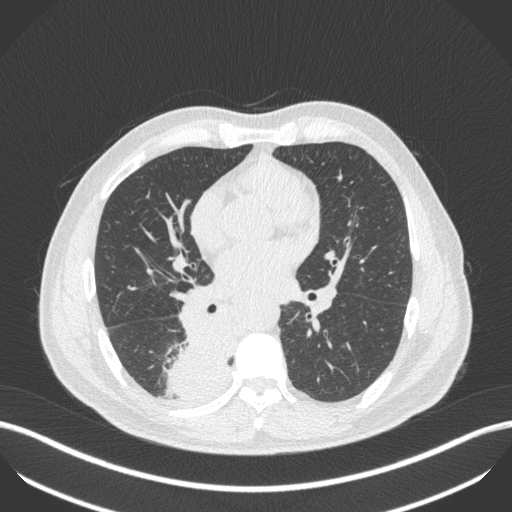
Chest CT, one axial slice. Position 235 of 451 along the scan axis. Reconstruction kernel B31f. 100 kVp. Lung window (W 1500 / L -600 HU). 512 × 512 image matrix. Male patient, age 61 years. From the clinical record (not read from this slice): clinical TNM (as recorded): T1 N0 M0.
Annotated regions visible in this slice (rectangle marked by the reading radiologist):
- lung tumour (recorded histology: small cell carcinoma): bounding box (x1, y1, x2, y2) in pixels: (157, 311, 239, 399)